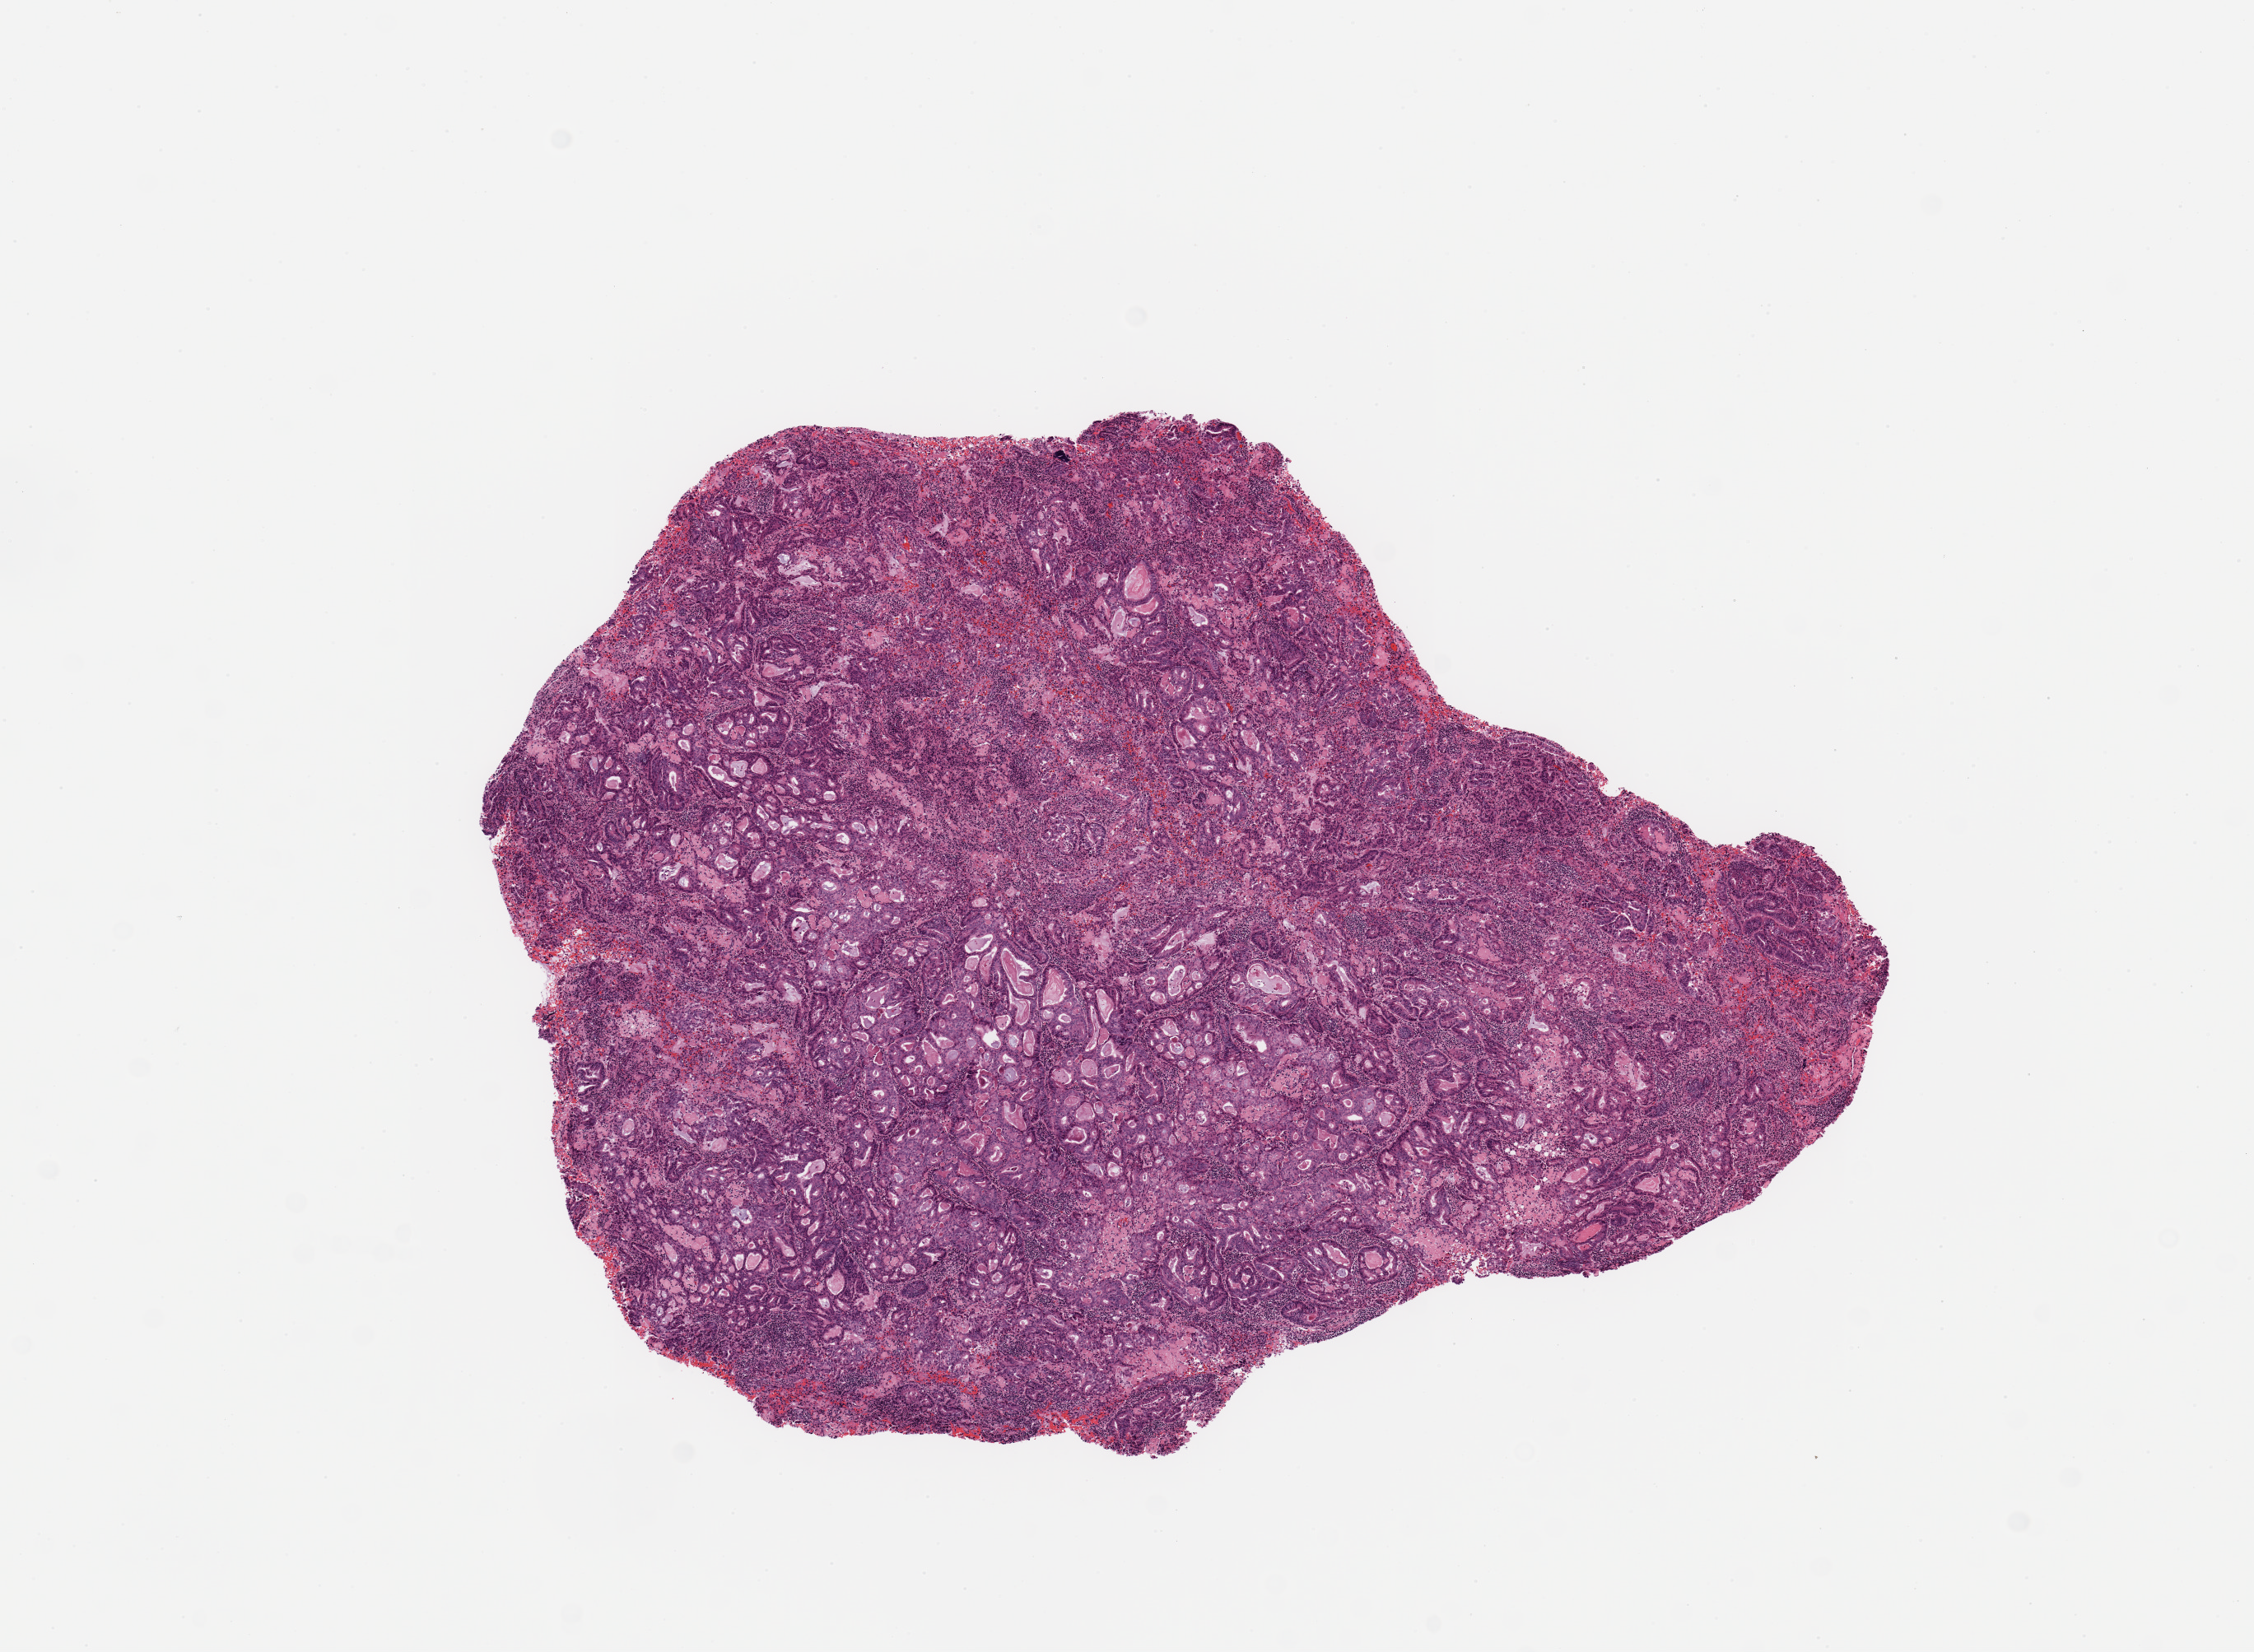
Whole-slide histology image, H&E-stained — shown as a low-resolution overview of the whole scanned area (about 10.8 x 7.9 mm, from a 20x scan). Tumour tissue sample, sampled site: uterus. Female, 74 y/o. Histologic grade: G3 (poorly differentiated). Composition of this section per pathologist review: tumour nuclei 90%, necrosis 2%.
AJCC pathologic stage: IV. Diagnosis: Endometrioid adenocarcinoma, NOS.